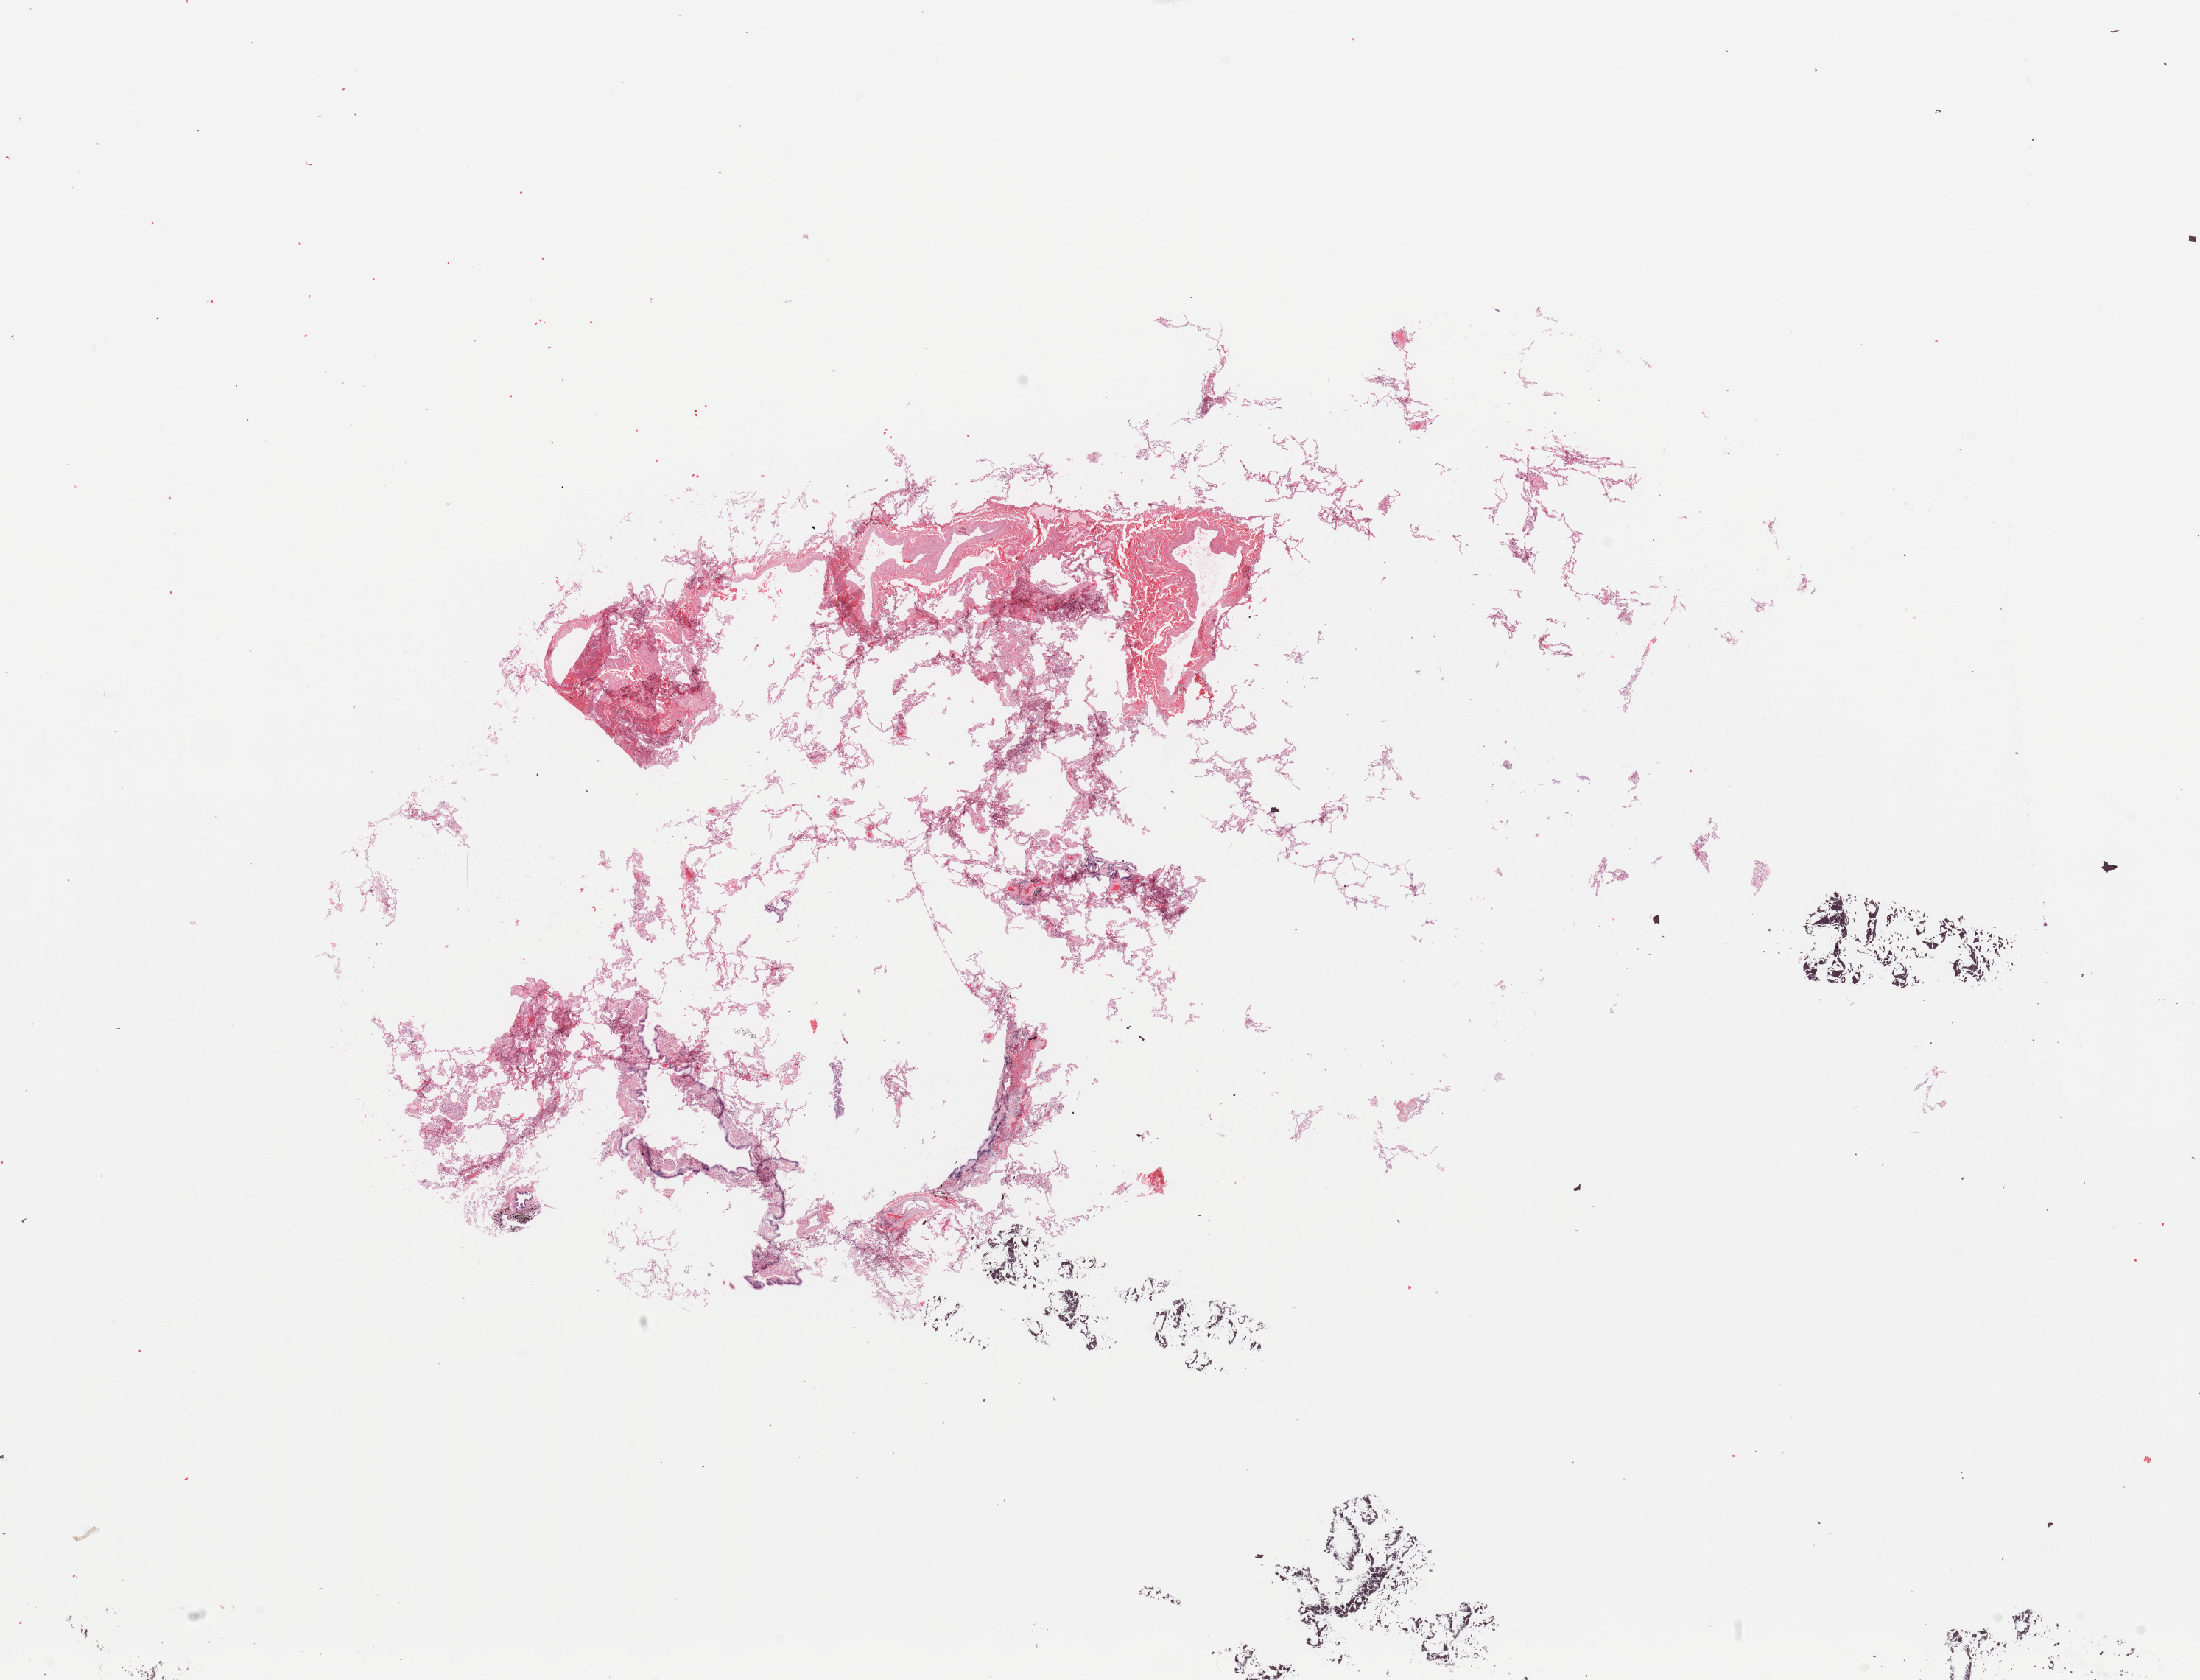
Digitized H&E tissue section (whole slide), whole scanned area (about 23.6 x 18.0 mm, slide scanned at 20x) shown as a low-resolution overview. Normal (non-tumour) tissue sample, sampled site: lung. Female, 50 y/o.
- this section: normal (non-tumour) tissue from the same patient
- patient diagnosis: Adenocarcinoma, NOS